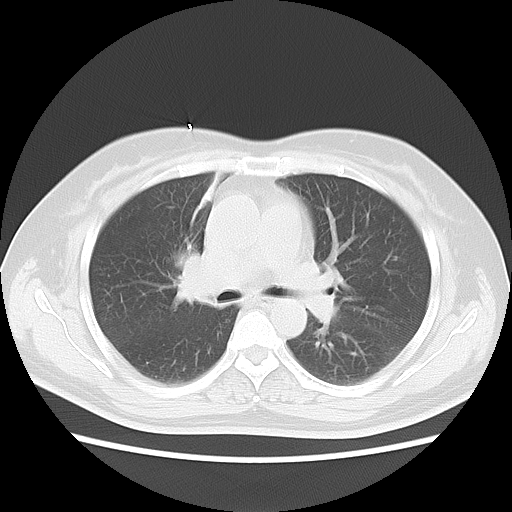
Chest CT, one axial slice; position 5 of 18 along the scan axis; reconstruction kernel LUNG; 120 kVp; lung window (W 1500 / L -600 HU); 5 mm slice thickness; 512 × 512 image matrix, field of view 350 × 350 mm. Female patient, age 54 years. Case-level facts recorded for this patient, not image findings: clinical TNM (as recorded): T2 N3 M0.
Annotated regions visible in this slice (rectangle marked by the reading radiologist):
- lung tumour (recorded histology: small cell carcinoma): bounding box <160,248,217,343> (left, top, right, bottom; pixels)